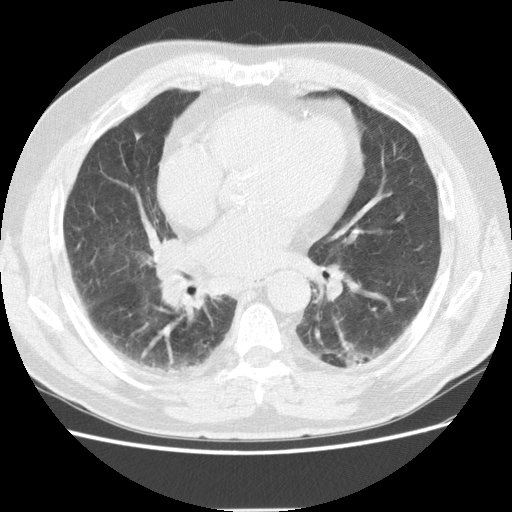
Chest CT (low-dose screening protocol), one axial image, first (baseline) screen, lung window (W 1500 / L -600 HU), standard (soft-tissue) reconstruction kernel (STANDARD). Male participant, aged 72 years at enrolment.
Lesion marked by an expert reader, bounding box <144,231,195,270> (left, top, right, bottom; pixels). No non-calcified nodule or mass ≥4 mm was recorded by the screening reader at this exam. Official screen result: negative screen, minor abnormalities not suspicious for lung cancer. Later outcome: lung cancer diagnosed 163 days after this screen — adenocarcinoma, NOS, right middle lobe, stage IIIB (AJCC 6th edition), 27 mm at pathology.